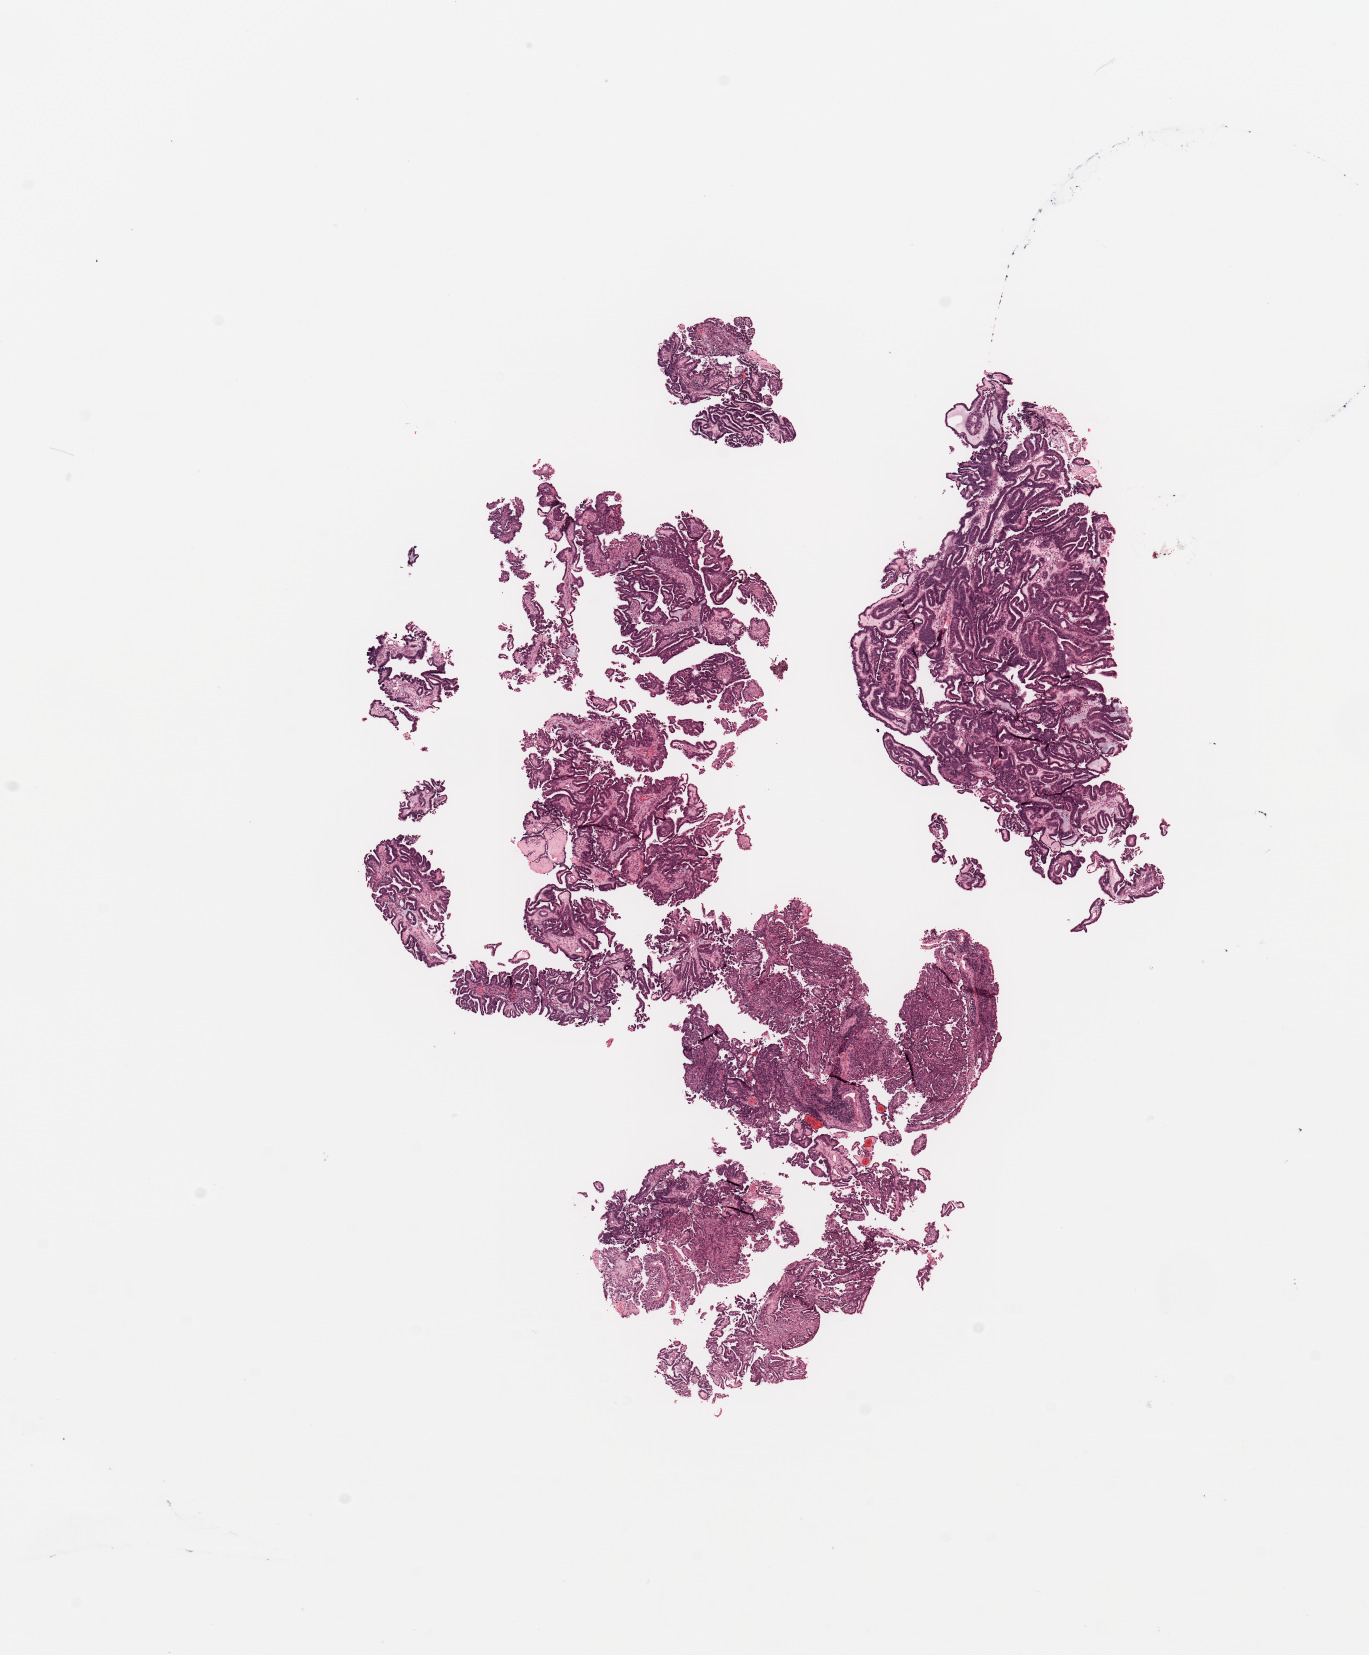
Whole-slide histology image, H&E-stained, whole scanned area (about 10.8 x 13.1 mm, slide scanned at 20x) shown as a low-resolution overview; tumour tissue sample, sampled site: uterus. Female, 58 y/o. Histologic grade: G3 (poorly differentiated). Pathologist review of this section (percent, as recorded): tumour nuclei 95%, necrosis 0%.
AJCC pathologic stage: IA. Histologic diagnosis: Endometrioid adenocarcinoma, NOS.